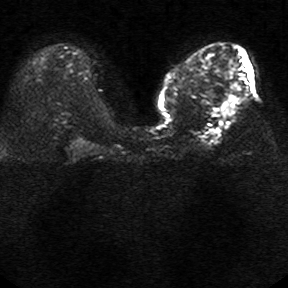
Breast MRI, one axial slice. Position 12 of 34 along the scan axis. Diffusion-weighted series; image 2 of 4 stored at this slice position (different b-values; order by instance number). 1.5 T. 5 mm slice thickness. 288 × 288 image matrix. Female patient.
Outlined on this slice (outlined manually by an expert reader):
- tumour on diffusion-weighted imaging: box from (x=230, y=96) to (x=237, y=103) px